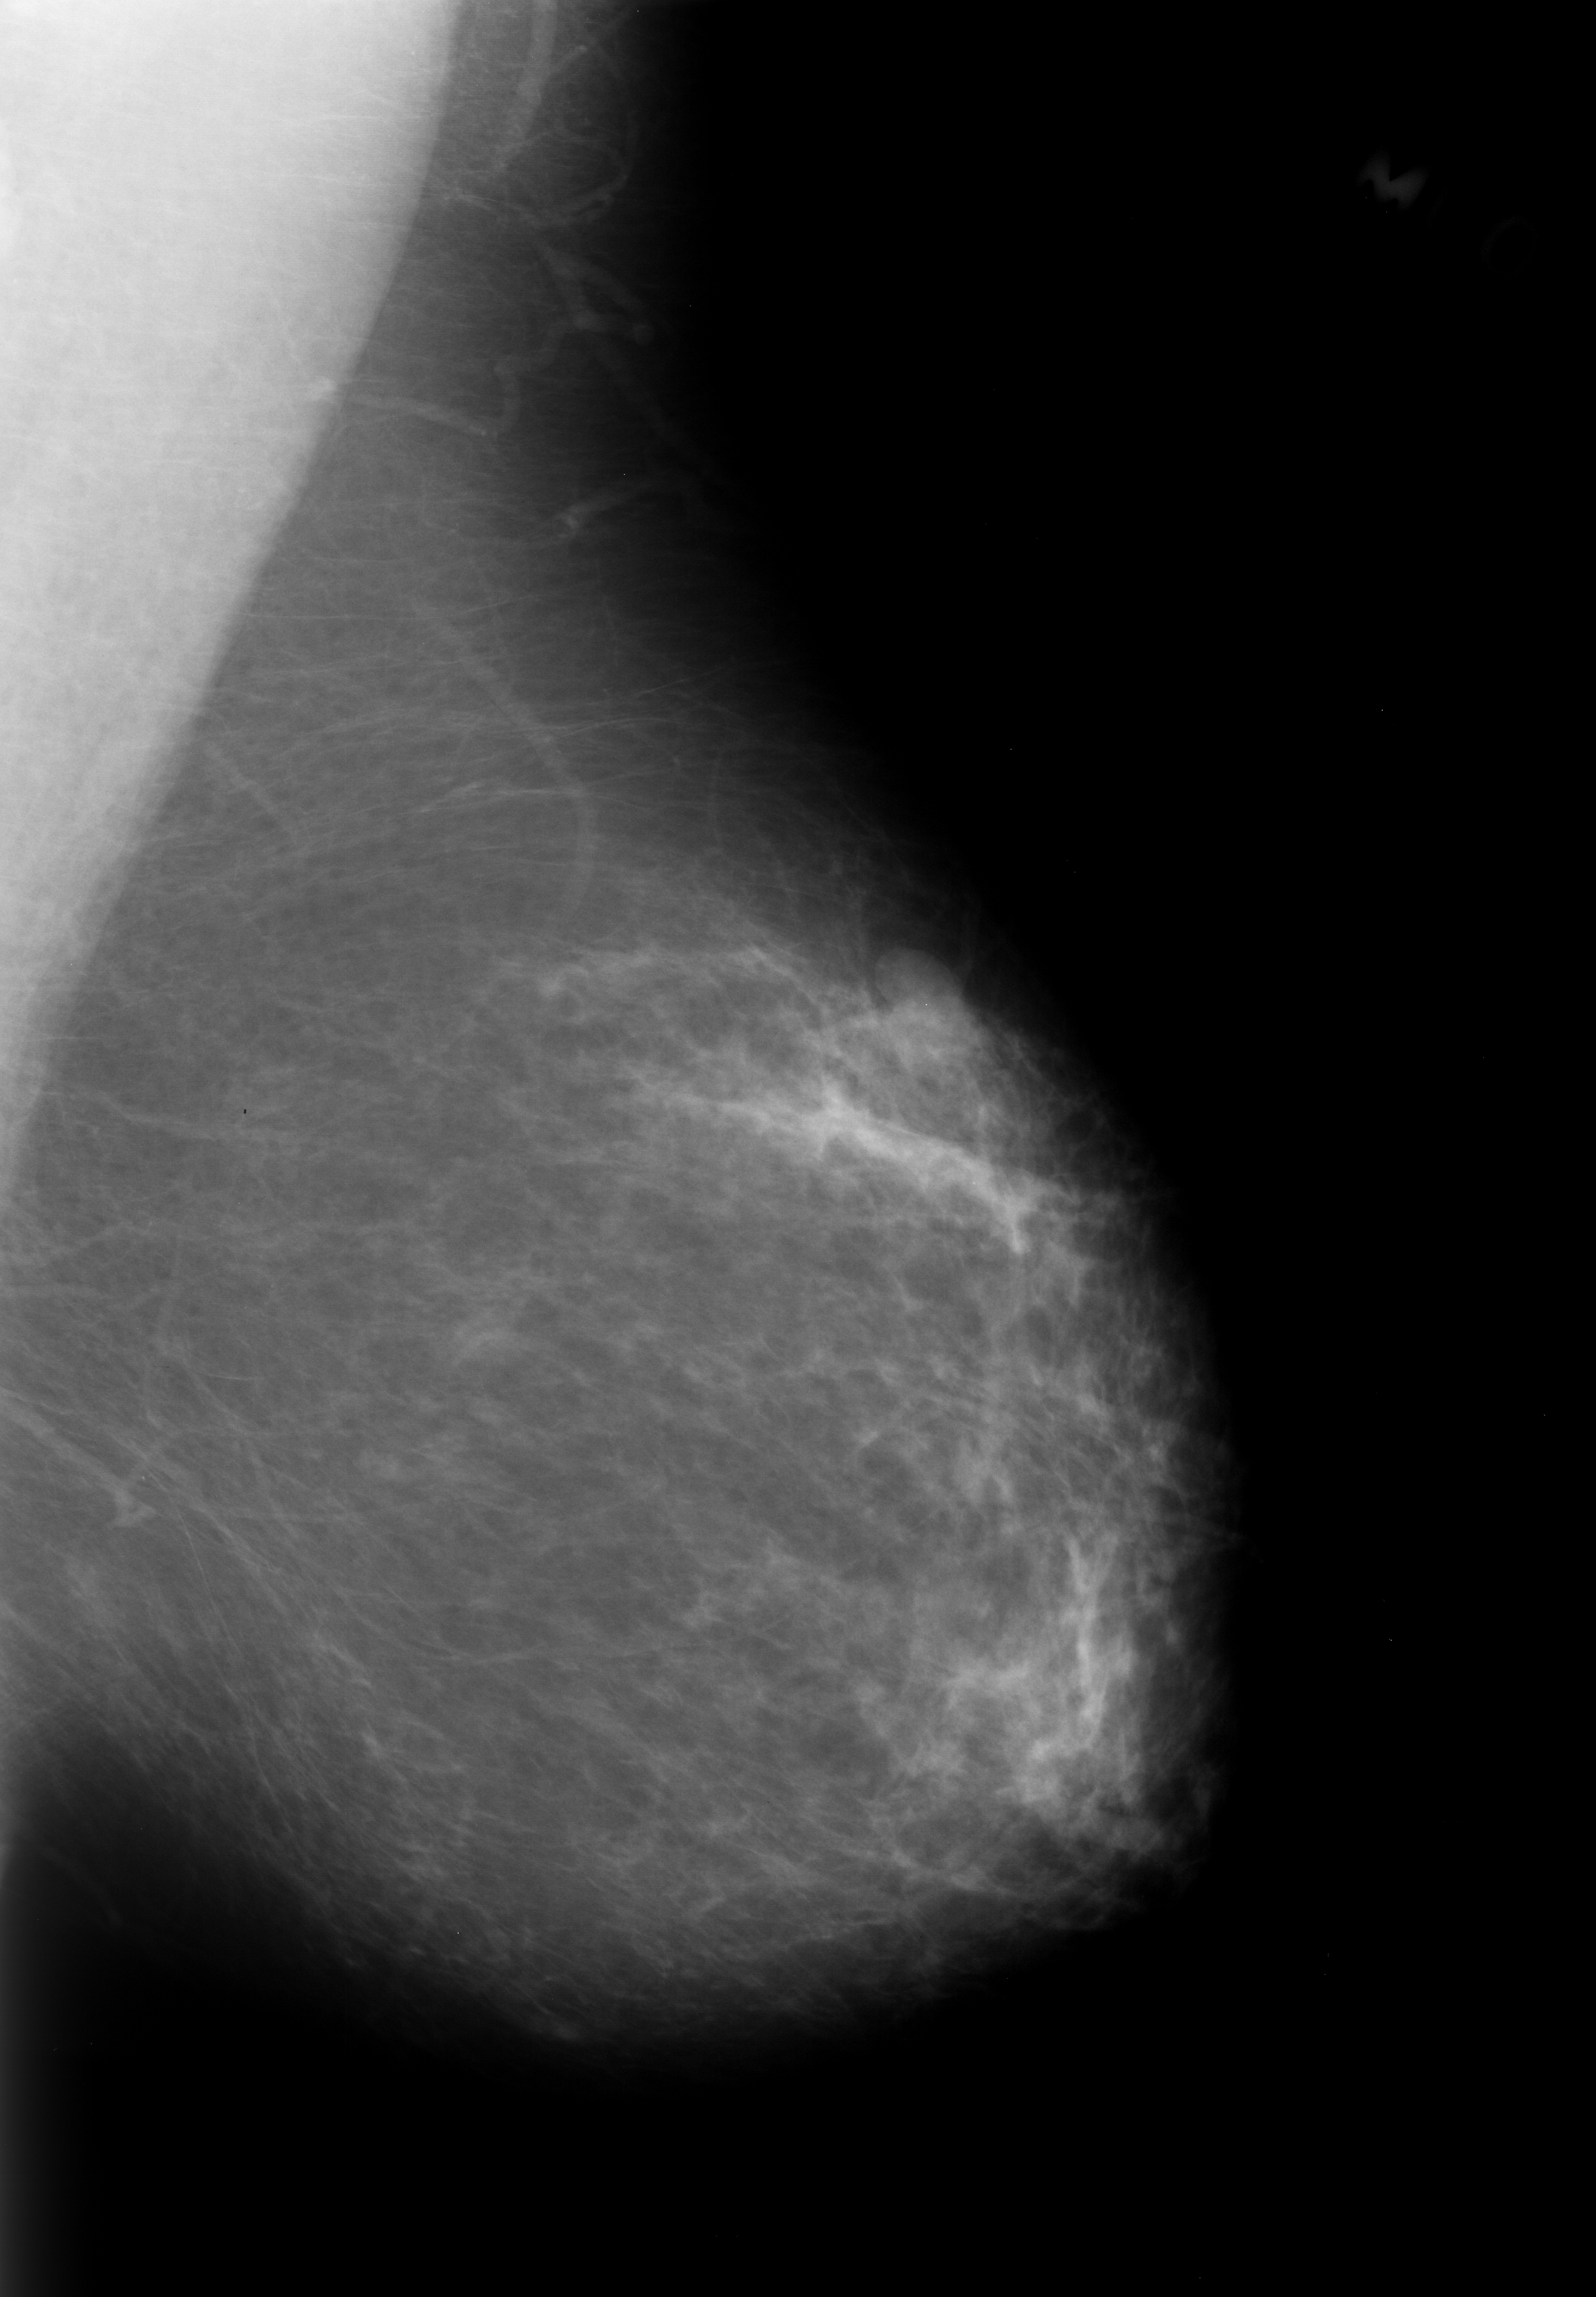
Digitized screen-film mammogram; left breast; MLO view; breast composition: almost entirely fatty (BI-RADS density category 1 of 4); 1596 × 2297 image matrix.
Expert-marked regions of interest on this image (one box per marked abnormality):
- mass, shape lobulated, margins obscured; BI-RADS assessment category 3; subtlety rating 5 on a 1 (subtle) to 5 (obvious) scale; pathology result (as recorded, not read from the image): benign: bounding box <860,956,995,1086> (left, top, right, bottom; pixels)